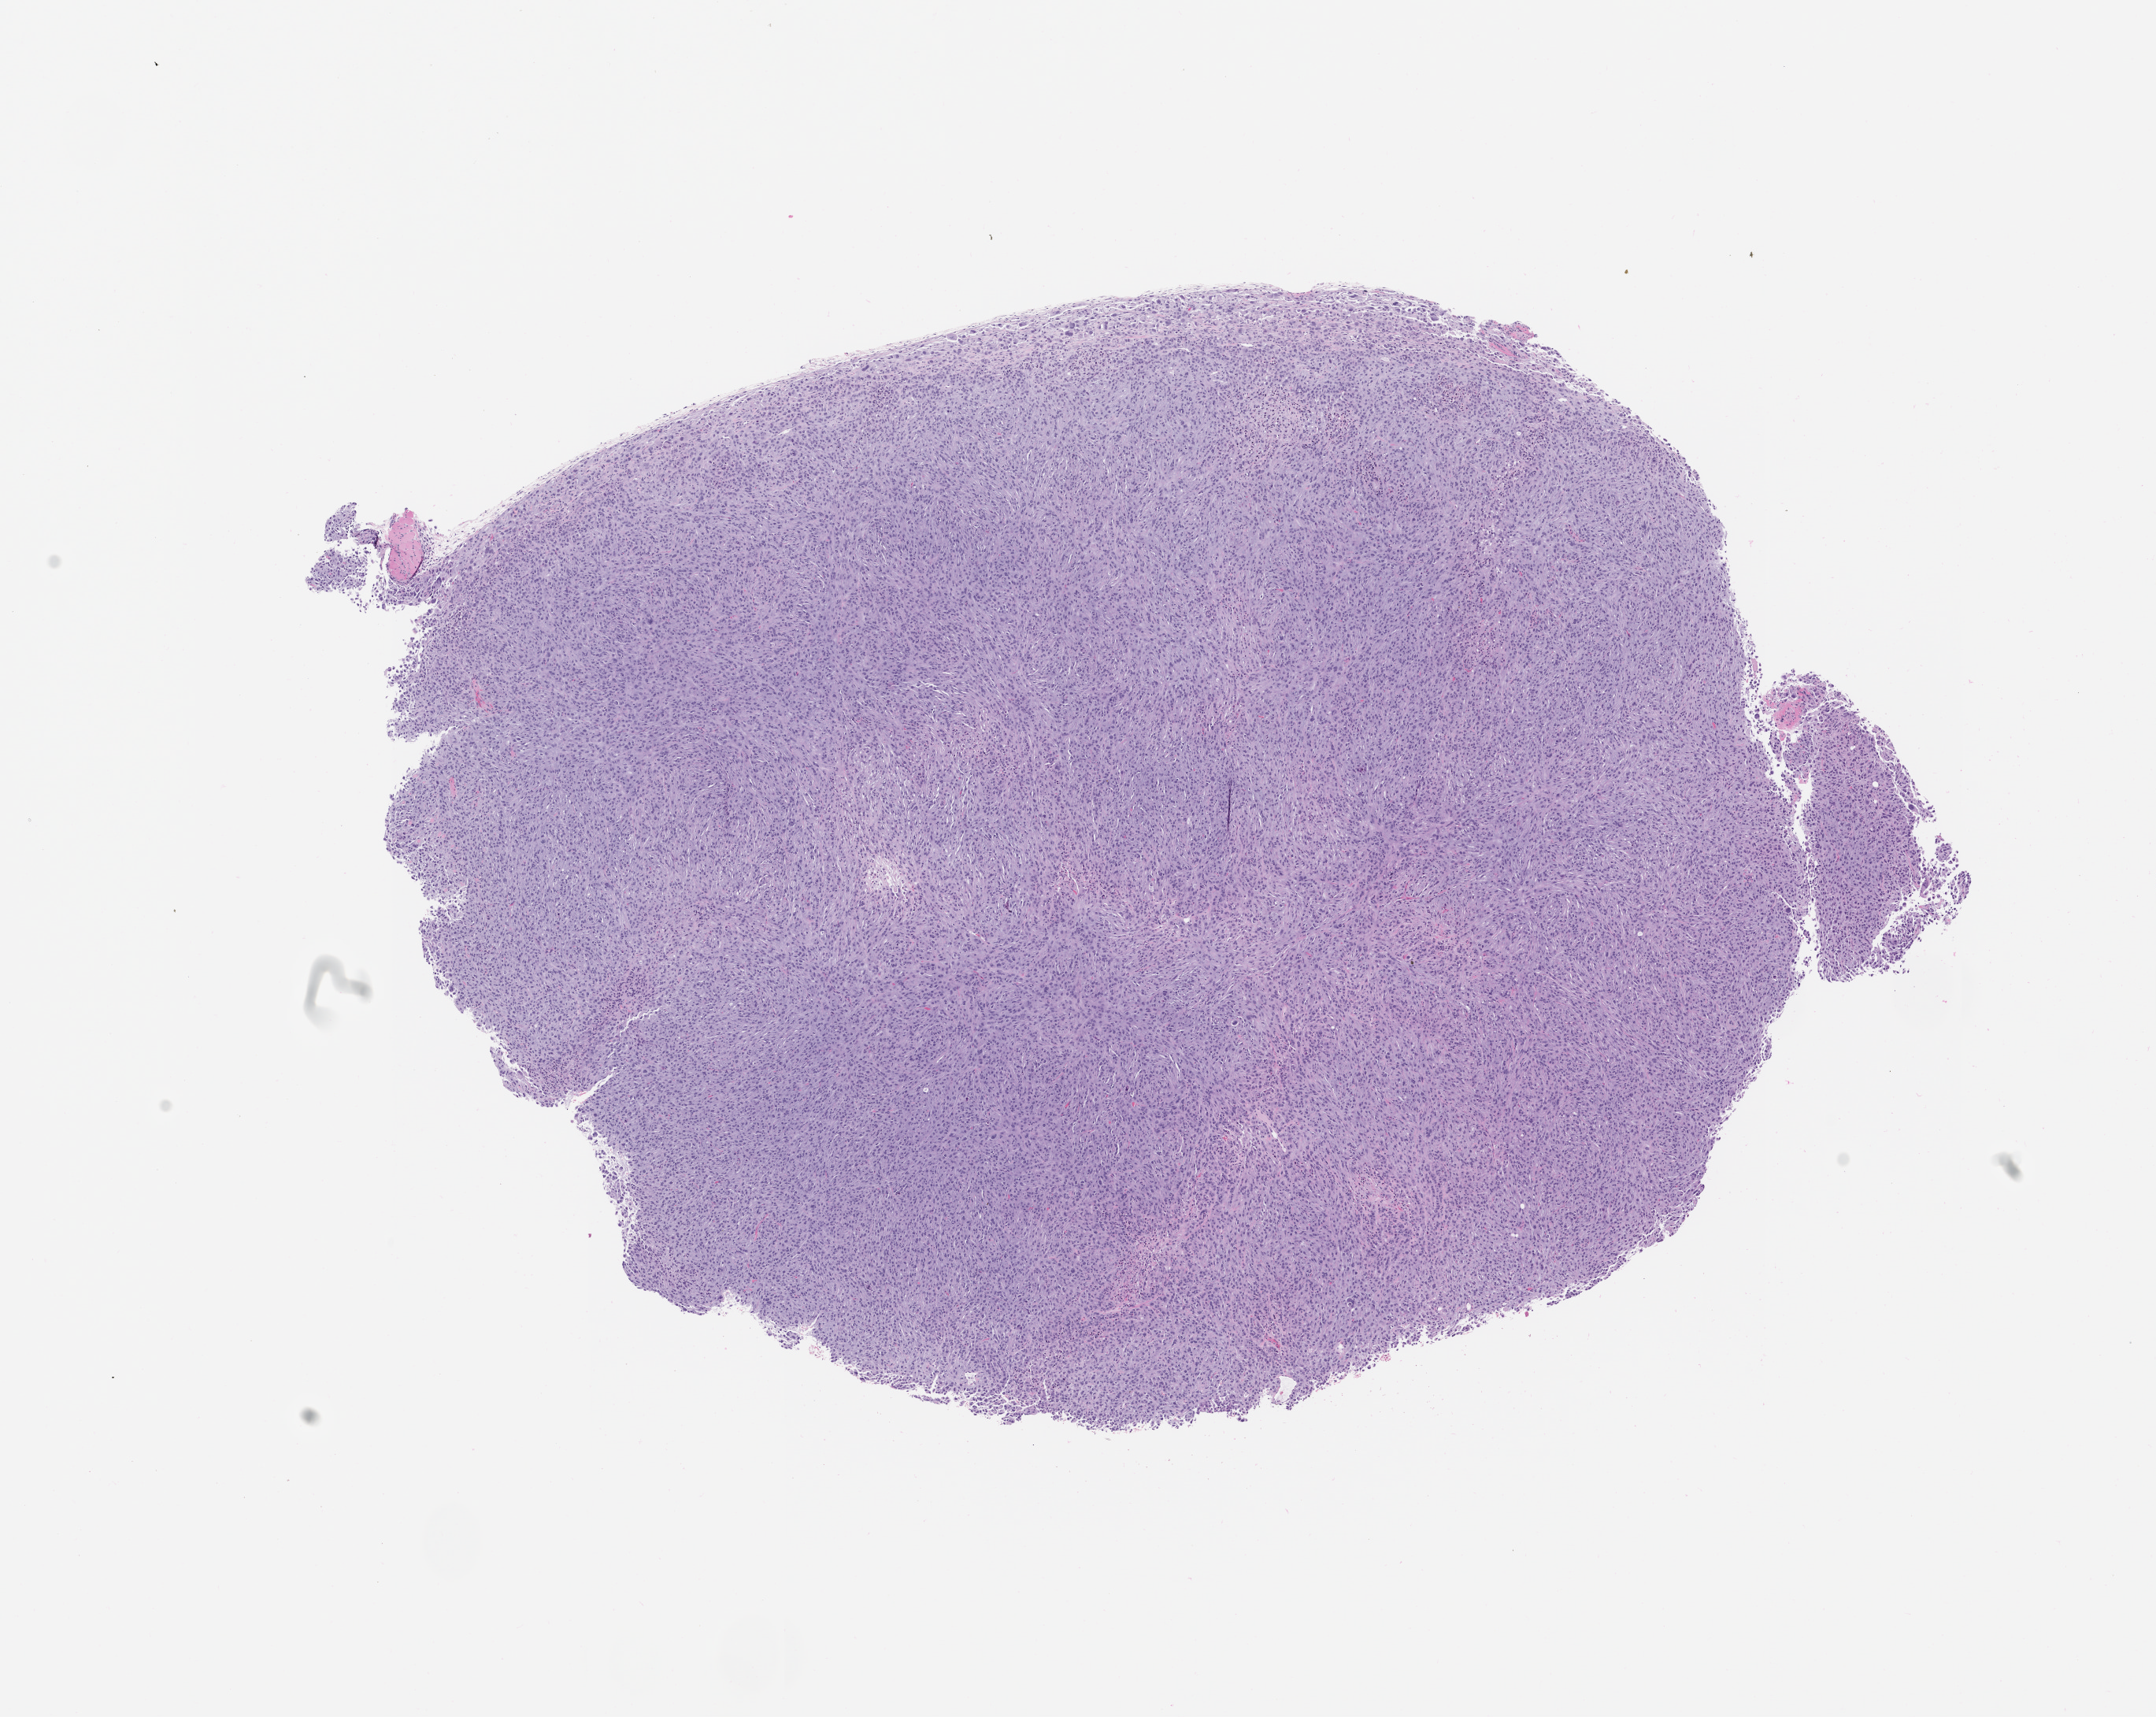
Whole-slide image, H&E: patient-derived xenograft (human tumor grown in a mouse), passage 1, a low-resolution overview of the entire scanned area, about 11.0 x 8.7 mm. Formalin-fixed, paraffin-embedded (FFPE) tissue. Tumor site category: thyroid.
Originating patient diagnosis: Thyroid Gland Oncocytic Carcinoma.